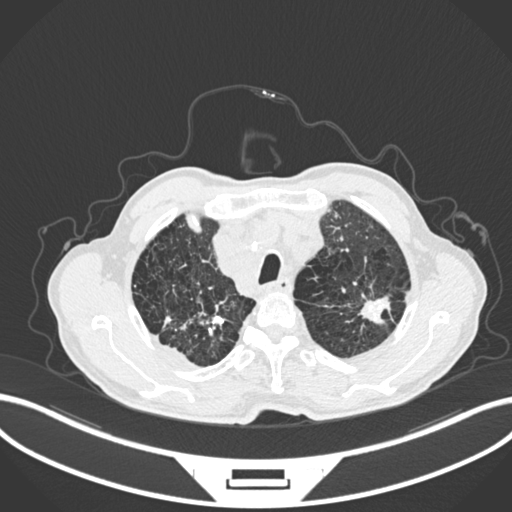
Chest CT, one axial slice. Slice 231 of 287 in the series (ordered by position). Reconstruction kernel B30f. Lung window (W 1500 / L -600 HU). 1 mm slice thickness. 512 × 512 image matrix. Patient: male, 74 years. Case-level facts recorded for this patient, not image findings: clinical TNM (as recorded): T2a N1 M0.
Annotated regions visible in this slice (bounding box drawn by a radiologist):
- lung tumour (recorded histology: adenocarcinoma): bounding box [x1, y1, x2, y2] px = [356, 294, 397, 329]